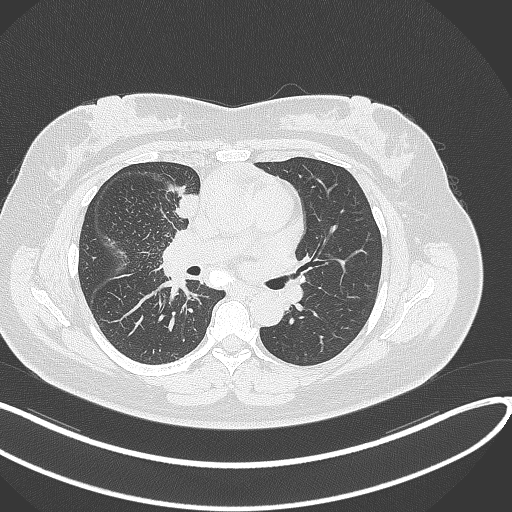
Chest CT, one axial slice. Reconstruction kernel B70f. Lung window (W 1500 / L -600 HU). 1 mm slice thickness. 512 × 512 image matrix. Patient: female, 46 years. From the clinical record (not read from this slice): clinical TNM (as recorded): T2a N1 M0.
Outlined on this slice (bounding box drawn by a radiologist):
- lung tumour (recorded histology: adenocarcinoma): bounding box (x1, y1, x2, y2) in pixels: (173, 193, 200, 223)